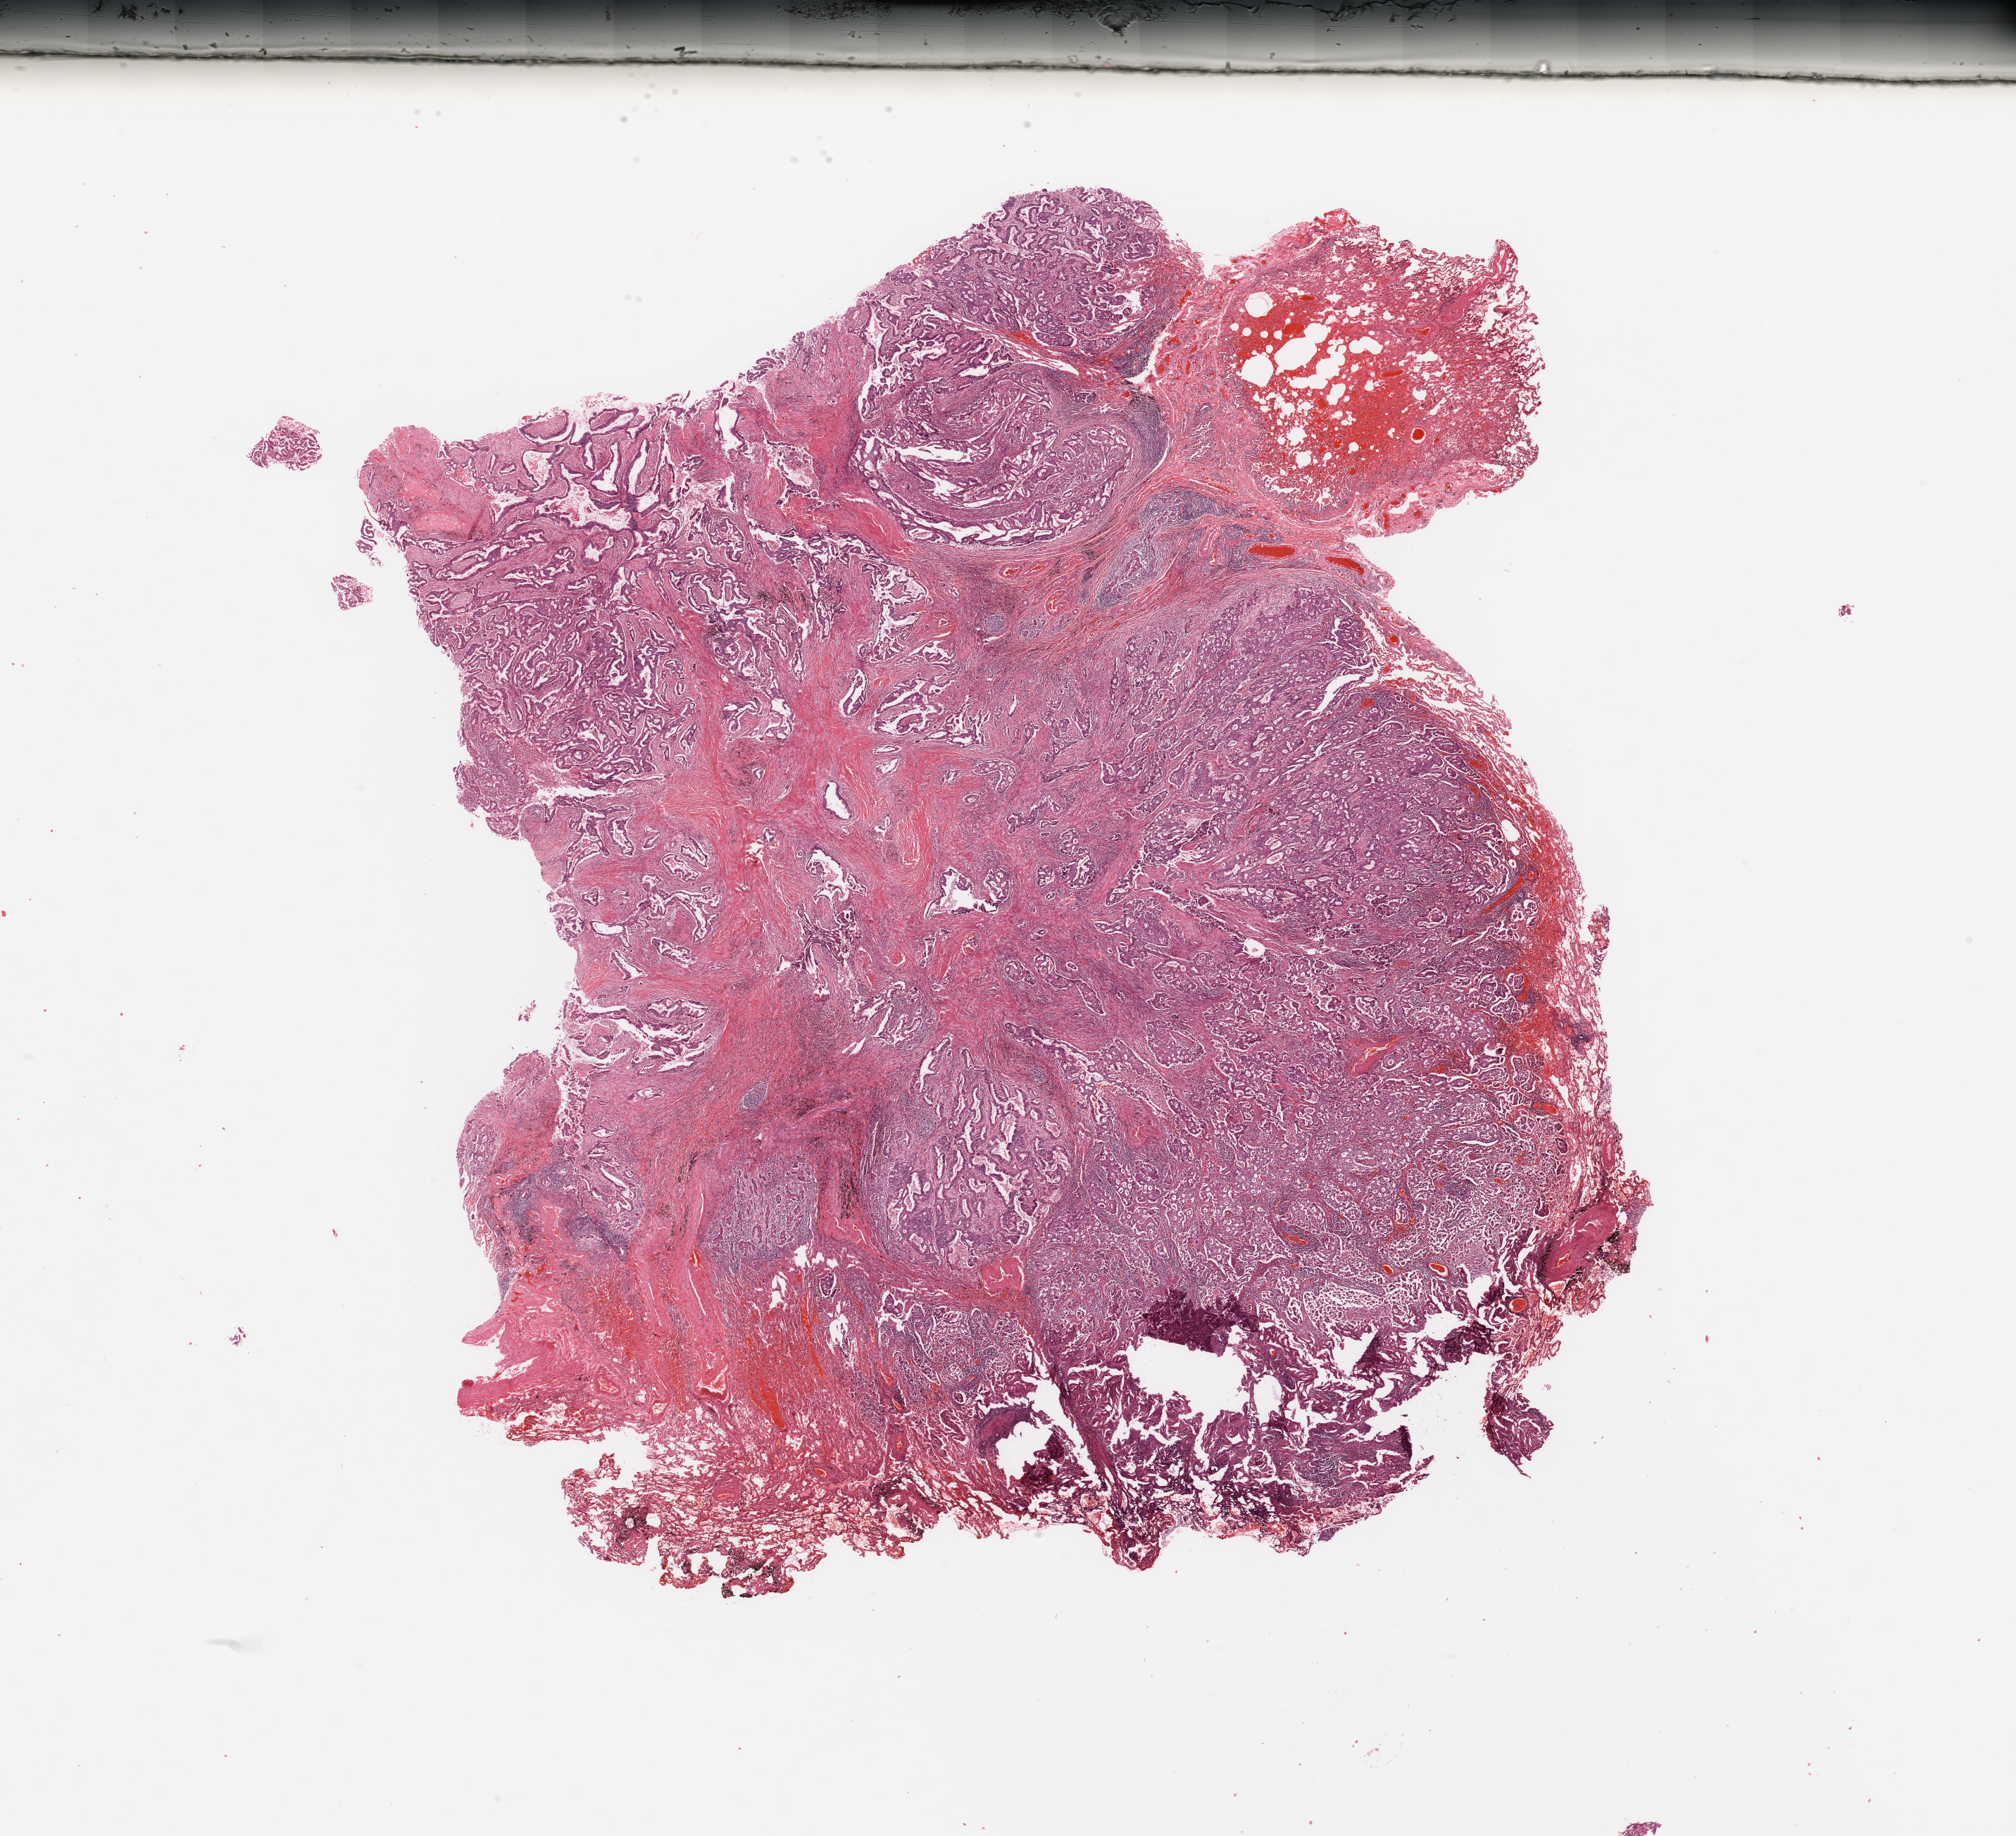
Hematoxylin and eosin (H&E) stained whole-slide image, shown as a low-resolution overview of the whole scanned area (about 22.6 x 20.6 mm), lung, tumour tissue. Patient: male, age 67 years. Histologic grade: G2 (moderately differentiated).
* diagnosis: Adenocarcinoma, NOS
* AJCC pathologic stage: IB